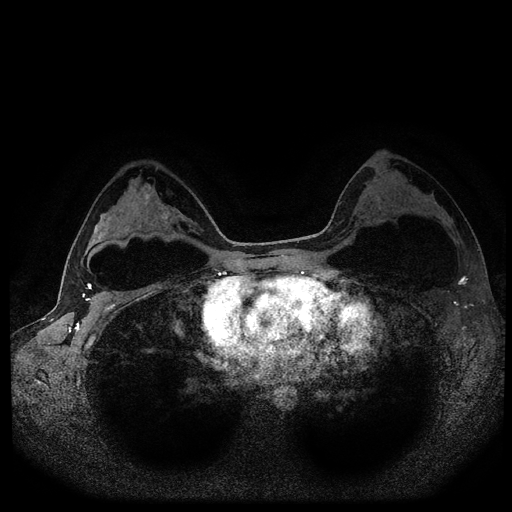
Breast MRI (dynamic contrast-enhanced, multi-phase), one axial slice; position 66 of 116 along the scan axis; dynamic contrast-enhanced series, time point 2 of 5 at this slice position (early post-contrast); 1.5 T; TE 2.6 ms, TR 5.4 ms; 2 mm slice thickness; 512 × 512 image matrix, field of view 340 × 340 mm. Female patient, age 33 years.
Annotated regions visible in this slice (semi-automatic segmentation, software-assisted and operator-edited):
- breast lesion (labelled benign in the annotation): bounding box (x1, y1, x2, y2) in pixels: (159, 210, 171, 224)
- breast lesion (labelled benign in the annotation): (144, 191, 152, 200)